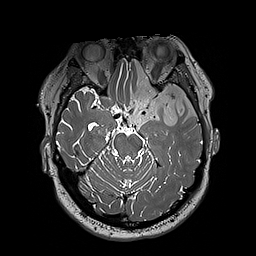
Brain MRI from a brain-tumour surgery series, one axial slice; slice 134 of 192 in the series (ordered by position); 1 mm slice thickness; 256 × 256 image matrix, field of view 250 × 250 mm. From the clinical record (not read from this slice): histopathology: Oligodendroglioma; WHO grade: 3.
Outlined on this slice (expert manual segmentation):
- tumour: bounding box [x1, y1, x2, y2] px = [124, 60, 197, 127]